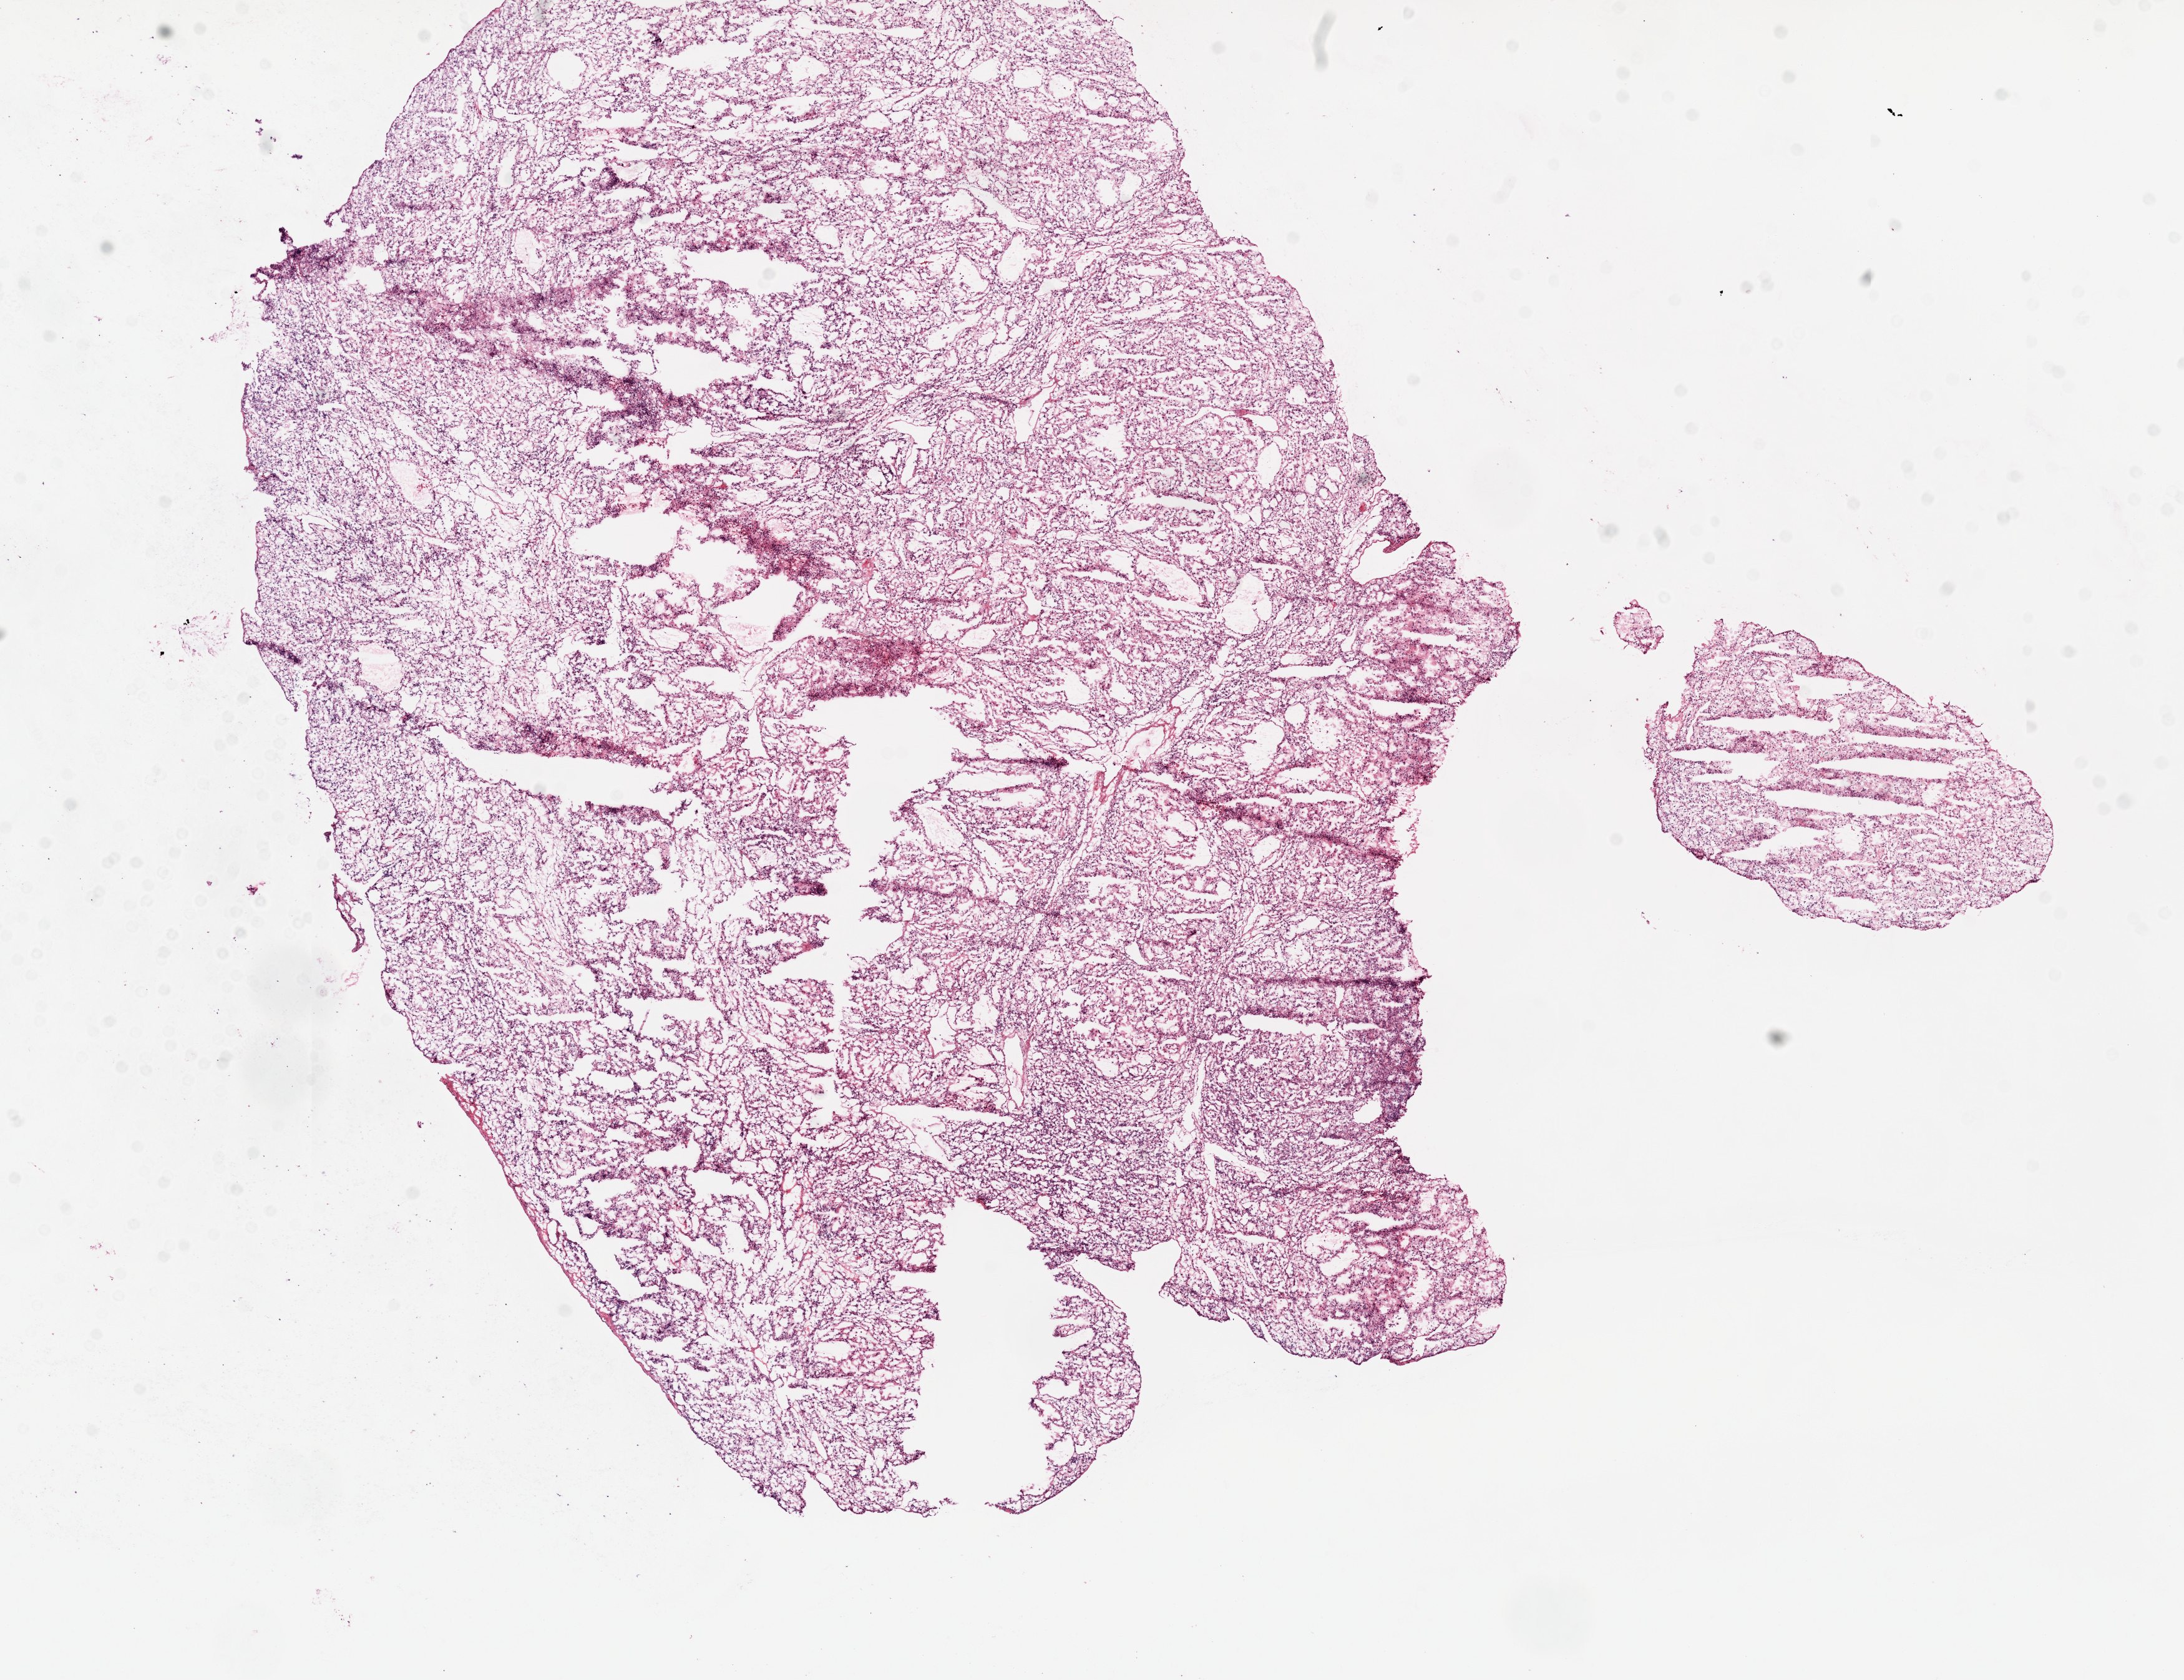
Digitized H&E tissue section (whole slide) — low-resolution overview of the scanned area, about 14.0 x 10.8 mm (acquisition: 20x scan). Frozen section from the top of the tissue portion. Kidney, primary tumour sample. Female patient; age at initial diagnosis 51 years. Histologic grade: G3 (poorly differentiated). Pathologist review of this section (percent, as recorded): tumour cells 90%, tumour nuclei 90%, normal cells 0%, stromal cells 10%, necrosis 0%.
- pathologic diagnosis: Clear cell adenocarcinoma, NOS
- AJCC pathologic stage: III
- lymph nodes positive (case pathology): 0 of 11 examined